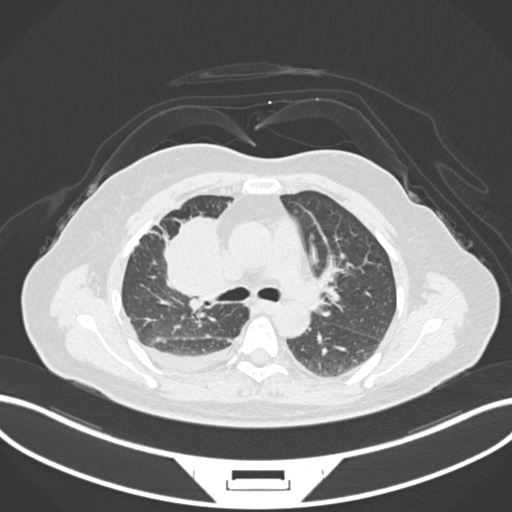
Chest CT, one axial slice. Slice 94 of 172 in the series (ordered by position). Reconstruction kernel B30f. 120 kVp. Lung window (W 1500 / L -600 HU). 1 mm slice thickness. 512 × 512 image matrix, field of view 400 × 400 mm. Female patient, age 52 years. From the clinical record (not read from this slice): clinical TNM (as recorded): T3 N1 M1.
Structures marked on this image (bounding box drawn by a radiologist):
- lung tumour (recorded histology: adenocarcinoma): box from (x=159, y=211) to (x=222, y=304) px